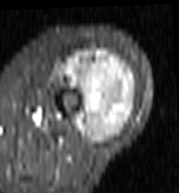
MRI of an extremity soft-tissue mass, one axial slice. STIR. MR volume resampled by the dataset authors to the PET/CT grid (not the native acquisition matrix). 179 × 193 image matrix, field of view 175 × 188 mm. Female patient. Case-level facts recorded for this patient, not image findings: histological type: undifferentiated – high grade; grade: high; site of the primary tumour: left thigh.
Outlined on this slice (expert contour drawn on MRI and transferred to this co-registered scan by the dataset authors):
- gross tumour volume including surrounding oedema: bounding box <54,50,138,143> (left, top, right, bottom; pixels)
- gross tumour volume (mass): <63,51,135,143>